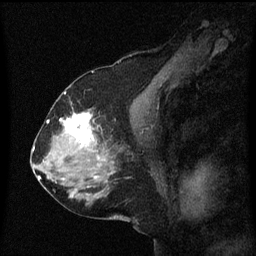
Breast MRI (dynamic contrast-enhanced), one sagittal slice; slice 32 of 60 in the series (ordered by position); dynamic contrast-enhanced series, image 2 of 3 at this slice position (ordered by acquisition); 1.5 T; TE 4.2 ms, TR 8.4 ms; 2 mm slice thickness; 256 × 256 image matrix, field of view 200 × 200 mm. Female patient, age 58 years.
Annotated regions visible in this slice (semi-automatic segmentation, software-assisted and operator-edited):
- analysis volume of interest (the breast-tissue region the enhancement analysis was run in; not a lesion): bounding box [x1, y1, x2, y2] px = [58, 110, 99, 151]
- tumour enhancement mask (voxels above the 70 % enhancement threshold inside the analysis volume of interest): [64, 112, 95, 145]